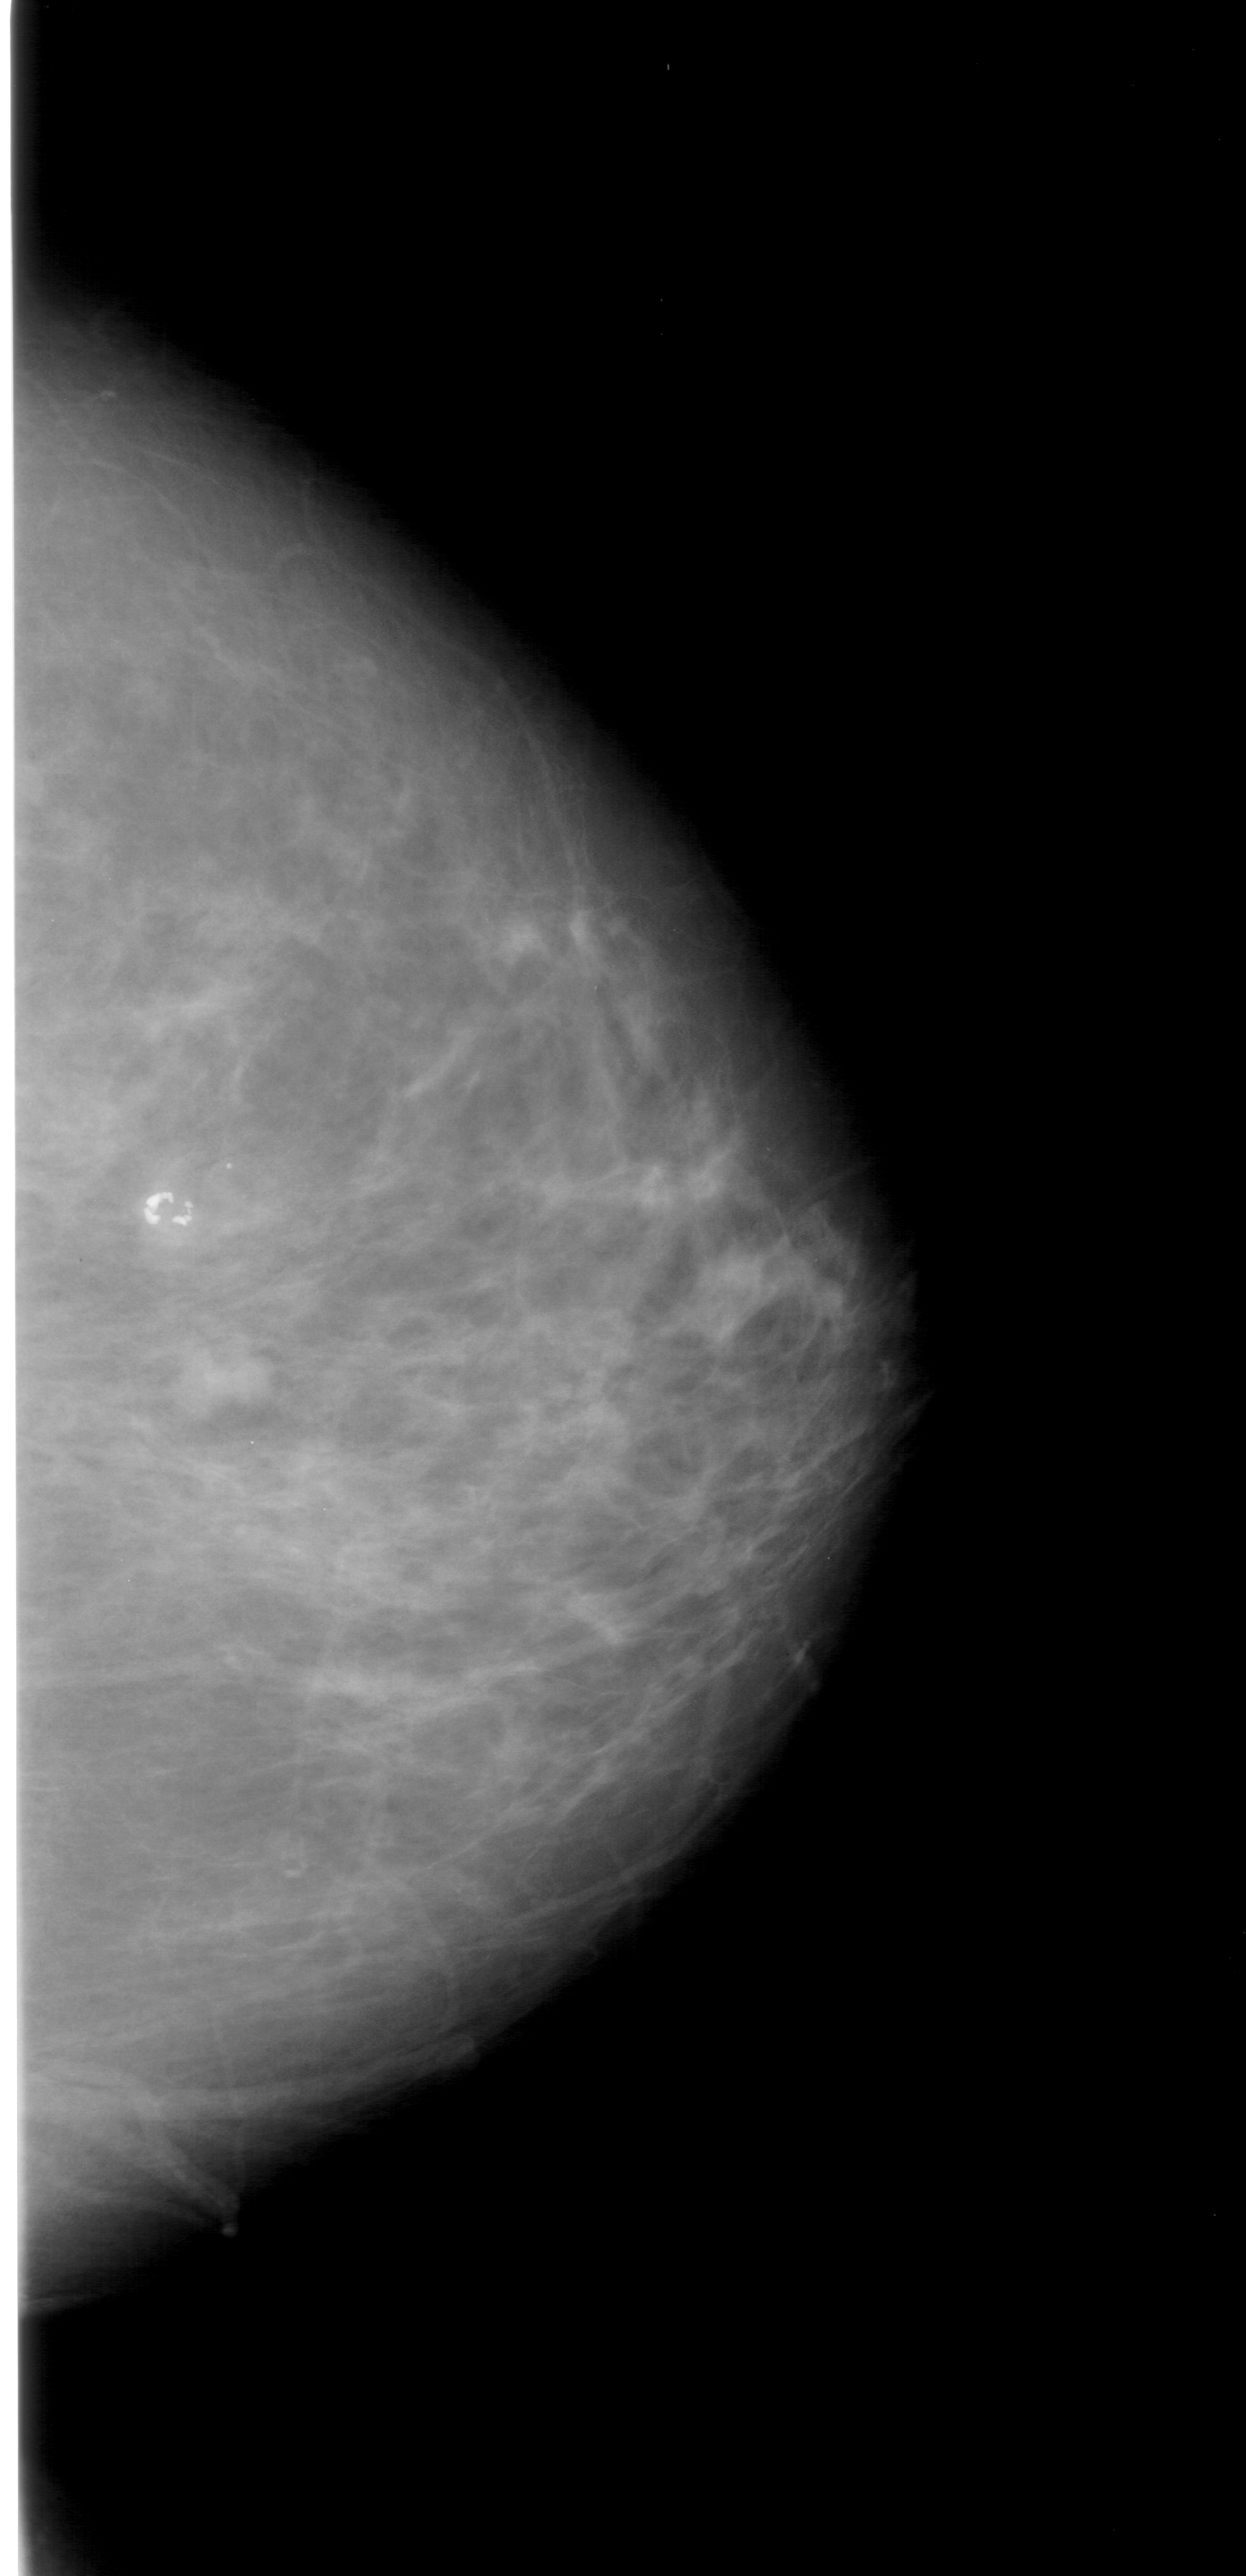
Digitized screen-film mammogram; right breast; craniocaudal (CC) view.
Abnormality record for this image: mass, shape lobulated, margins ill defined; BI-RADS assessment category 4; subtlety rating 1 on a 1 (subtle) to 5 (obvious) scale; pathology (as recorded): malignant.